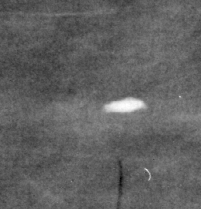
Crop from a digitized film mammogram around one marked abnormality; right breast; MLO view; BI-RADS breast density category 1 (scale 1–4).
Marked abnormality: calcifications, morphology vascular; BI-RADS assessment category 2; benign without callback (not worked up further).